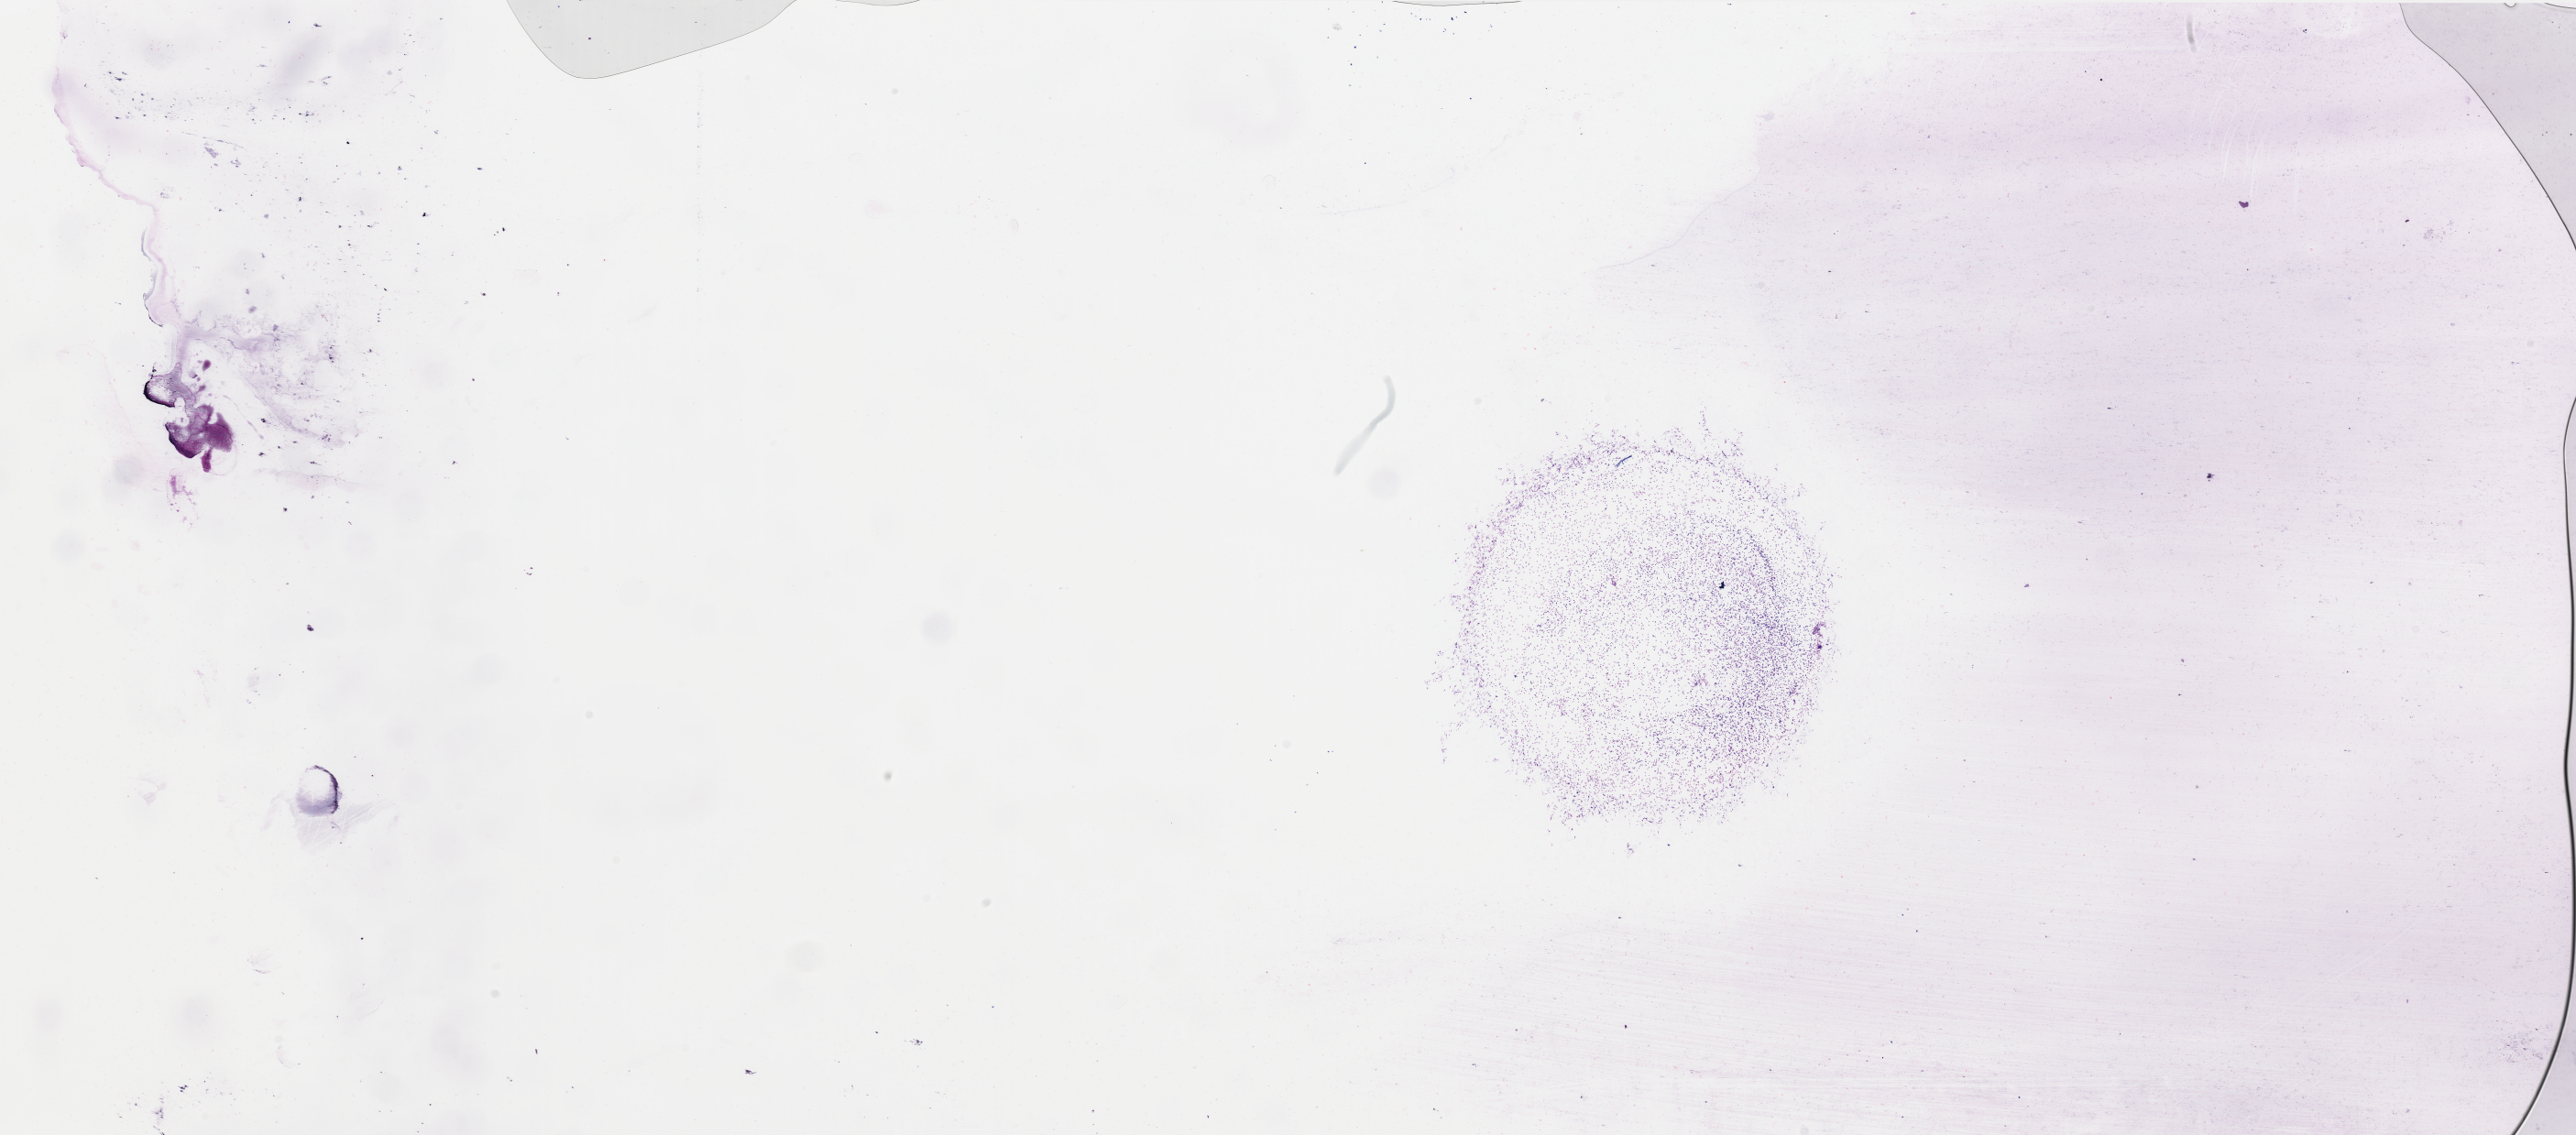
H&E-stained whole-slide image, a low-resolution overview of the entire scanned area, about 44.4 x 19.6 mm (from a 40x scan), peripheral blood (leukaemic) sample. Female, 69 y/o. Blasts: 75%.
* WHO classification: AML not otherwise specified
* diagnosis: Acute Myeloid Leukemia